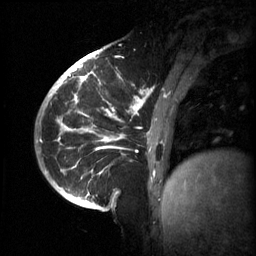
Breast MRI (dynamic contrast-enhanced), one sagittal slice; position 17 of 60 along the scan axis; 3 images stored at this slice position (order not interpretable as contrast timing); 1.5 T; TE 4.2 ms, TR 11 ms; 2 mm slice thickness; 256 × 256 image matrix, field of view 220 × 220 mm. Female patient, age 51 years.
Outlined on this slice (semi-automatically segmented with operator editing):
- analysis volume of interest (the breast-tissue region the enhancement analysis was run in; not a lesion): box from (x=63, y=80) to (x=187, y=201) px
- tumour enhancement mask (voxels above the 70 % enhancement threshold inside the analysis volume of interest): (x=68, y=80)–(x=154, y=183)